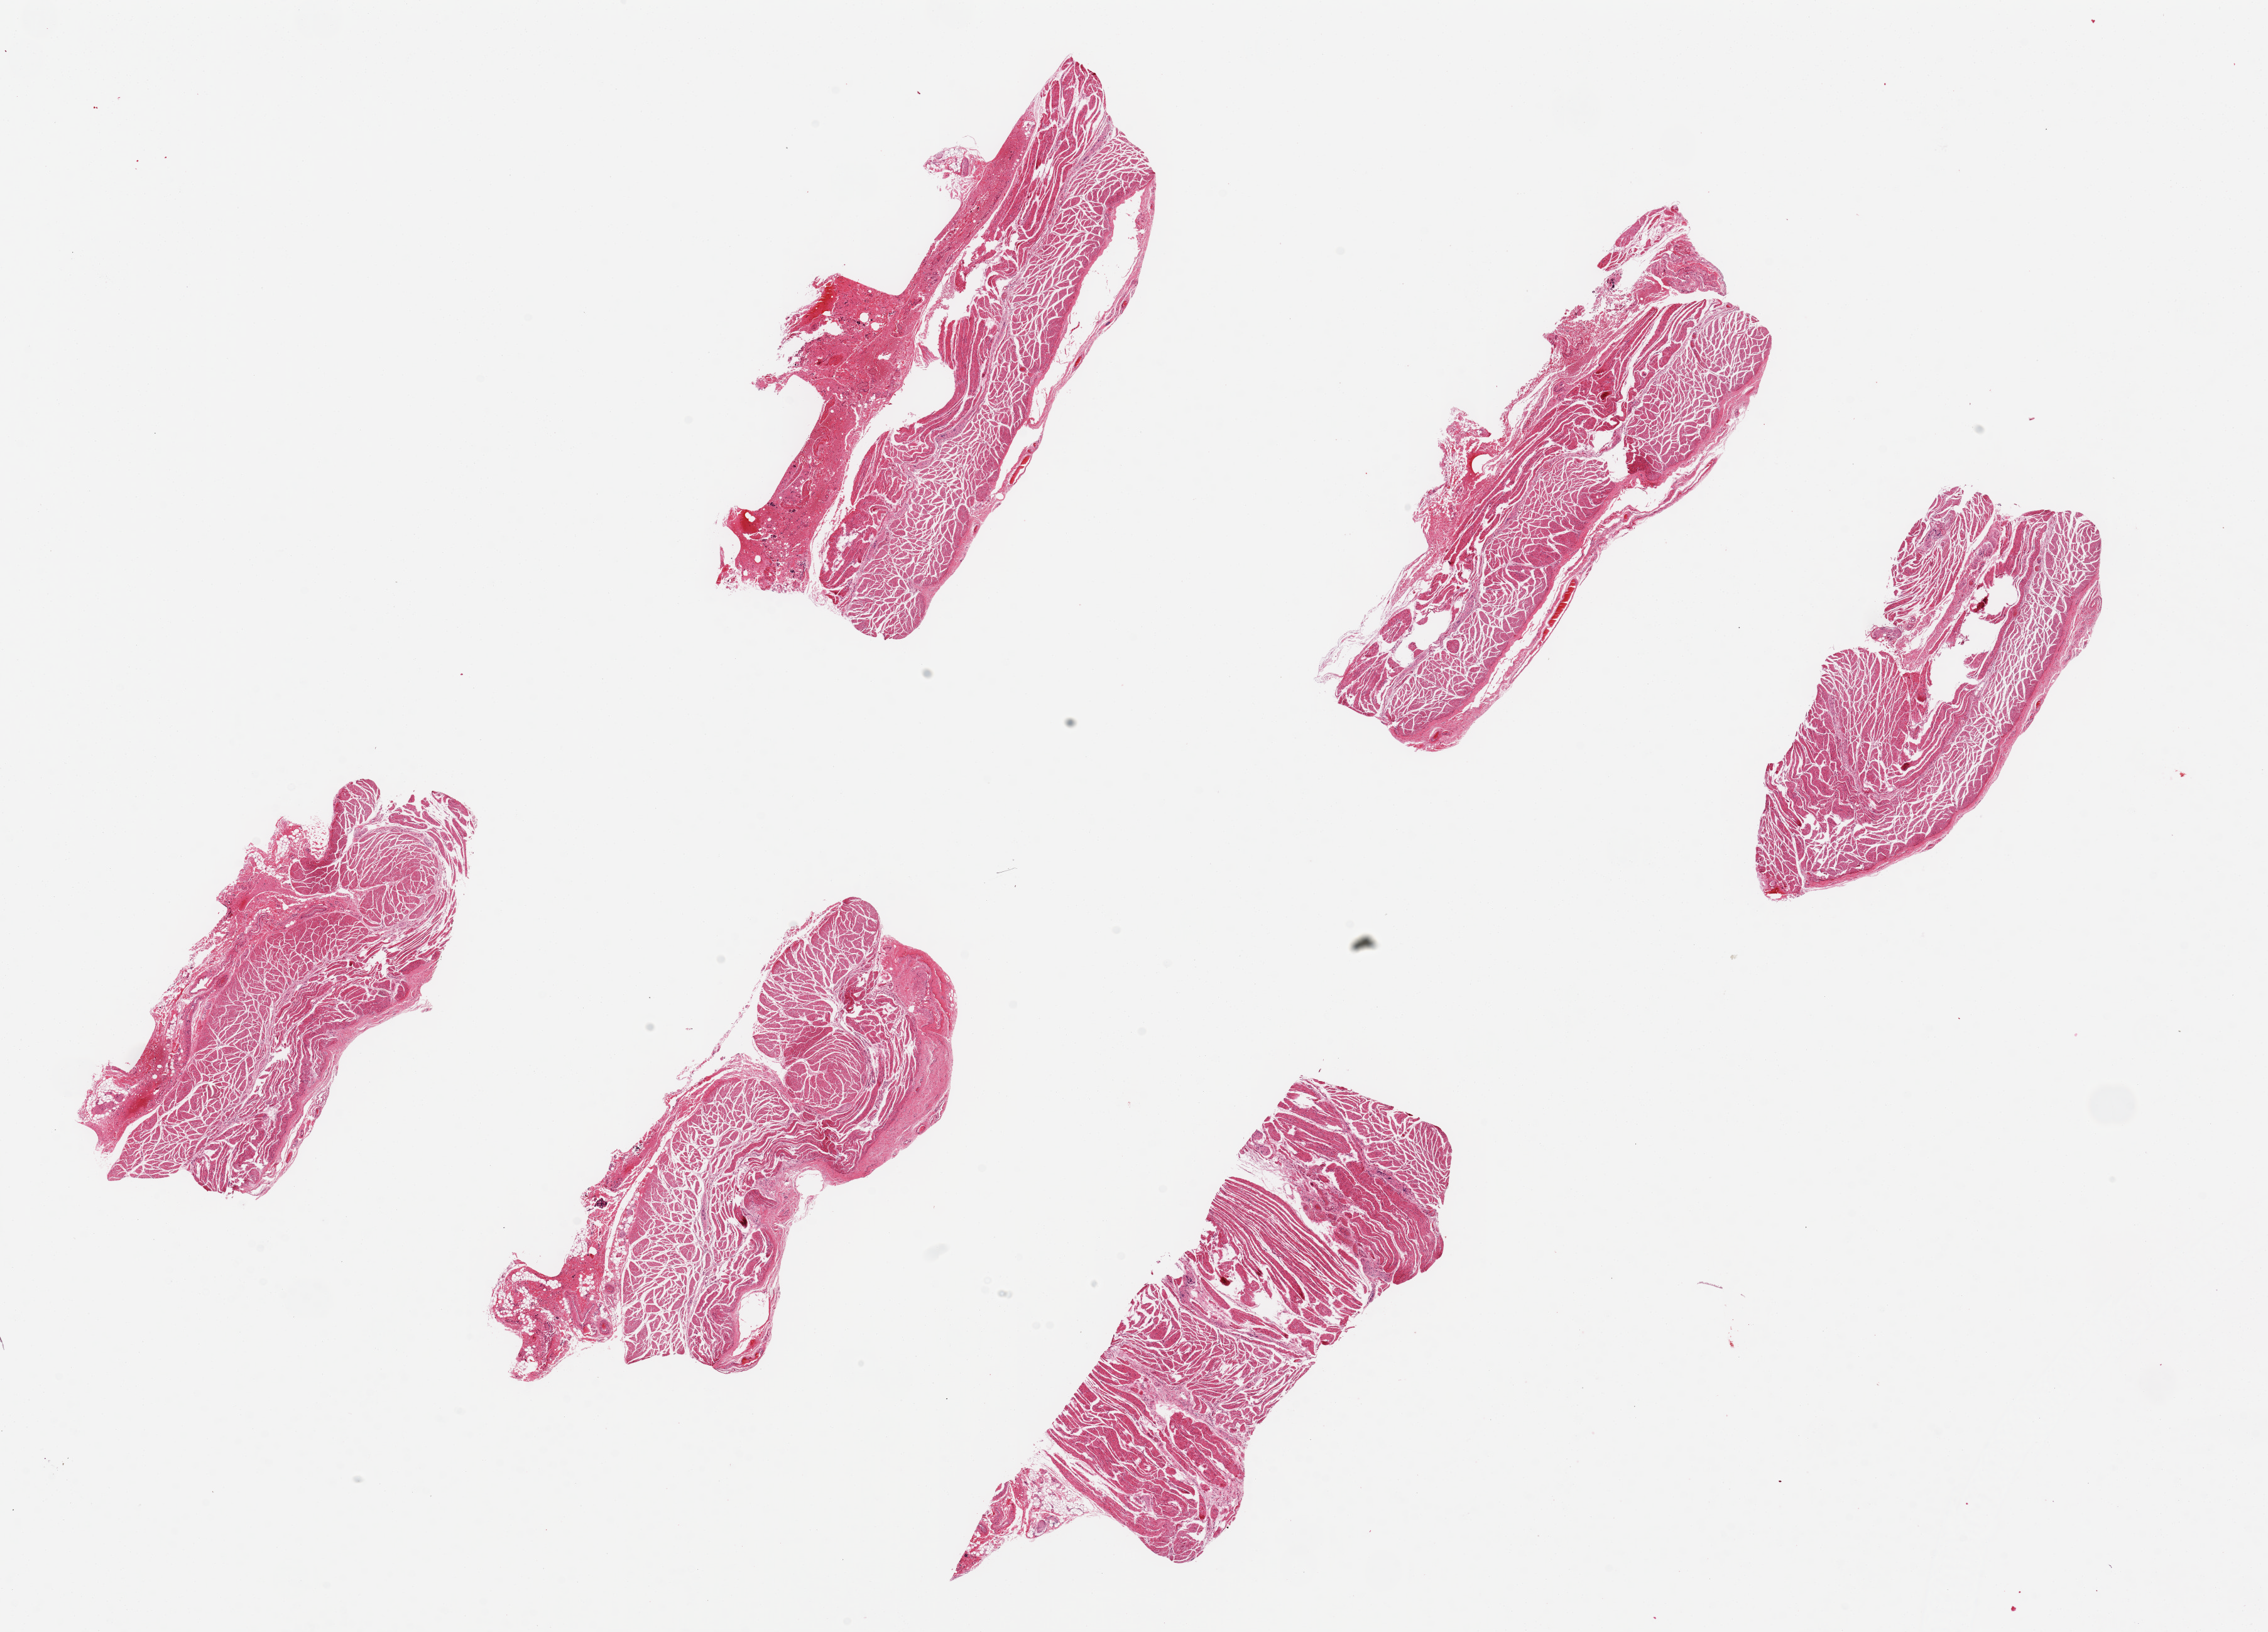
Haematoxylin and eosin whole-slide image — whole scanned area (about 28.5 x 20.5 mm, from a 20x scan) shown as a low-resolution overview; PAXgene-fixed, paraffin-embedded tissue; target tissue: esophageal muscle; donor tissue sample. Donor sex: female.
Reviewer comment on this tissue sample: 6 pieces up to 7x3 mm.